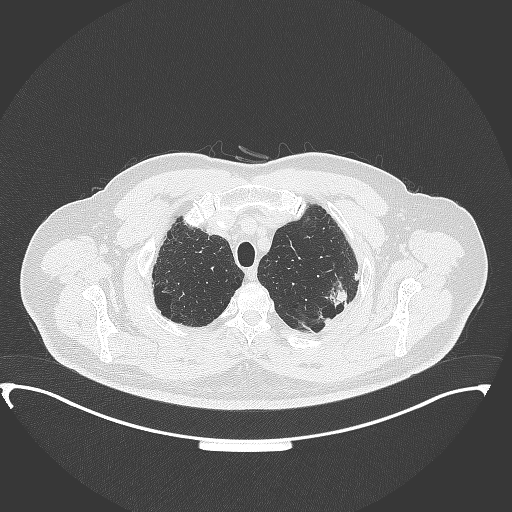
Chest CT, one axial slice; slice 313 of 350 in the series (ordered by position); reconstruction kernel B70f; 120 kVp; lung window (W 1500 / L -600 HU); 1 mm slice thickness; 512 × 512 image matrix, field of view 459 × 459 mm. Male patient, age 64 years. From the clinical record (not read from this slice): clinical TNM (as recorded): T1c N1 M1.
Structures marked on this image (rectangle marked by the reading radiologist):
- lung tumour (recorded histology: adenocarcinoma): bounding box (x1, y1, x2, y2) in pixels: (327, 274, 351, 311)